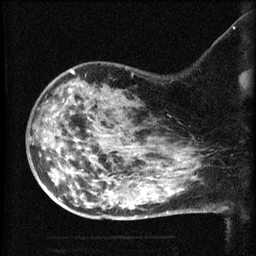
Breast MRI (dynamic contrast-enhanced), one sagittal slice; position 43 of 60 along the scan axis; dynamic contrast-enhanced series, image 2 of 3 at this slice position (ordered by acquisition); 1.5 T; TE 4.2 ms, TR 8.2 ms; 2.1 mm slice thickness; 256 × 256 image matrix, field of view 180 × 180 mm. Female patient, age 50 years.
Structures marked on this image (semi-automatically segmented with operator editing):
- analysis volume of interest (the breast-tissue region the enhancement analysis was run in; not a lesion): bounding box (x1, y1, x2, y2) in pixels: (38, 75, 169, 211)
- tumour enhancement mask (voxels above the 70 % enhancement threshold inside the analysis volume of interest): (122, 206, 125, 209)